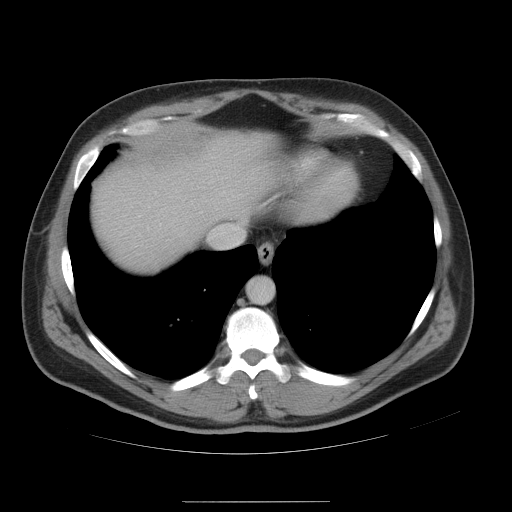
Contrast-enhanced abdominal CT, one axial slice; position 46 of 54 along the scan axis; intravenous contrast given; soft-tissue window (W 400 / L 40 HU); 5 mm slice thickness; 512 × 512 image matrix. Male patient, age 40 years. From the clinical record (not read from this slice): diagnosis: colorectal cancer liver metastases, imaged before liver resection; multiple liver metastases: no; largest metastasis: 15 cm; chemotherapy before resection: no.
Annotated regions visible in this slice (outlined manually by an expert reader):
- hepatic veins: bounding box <209,225,240,245> (left, top, right, bottom; pixels)
- liver: <92,131,287,275>
- planned liver remnant (the part of the liver to remain after resection): <170,131,287,249>